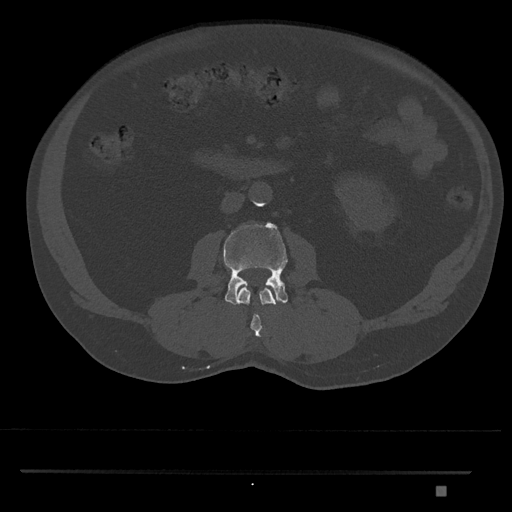
CT including the spine, one axial slice; position 709 of 1134 along the scan axis; 120 kVp; bone window (W 1800 / L 400 HU); 512 × 512 image matrix, field of view 429 × 429 mm. Patient: male, 65 years. From the clinical record (not read from this slice): primary cancer: prostate.
Structures marked on this image (semi-automatic segmentation, software-assisted and operator-edited):
- L2 vertebra: bounding box (x1, y1, x2, y2) in pixels: (238, 286, 276, 337)
- L3 vertebra: (223, 222, 288, 305)